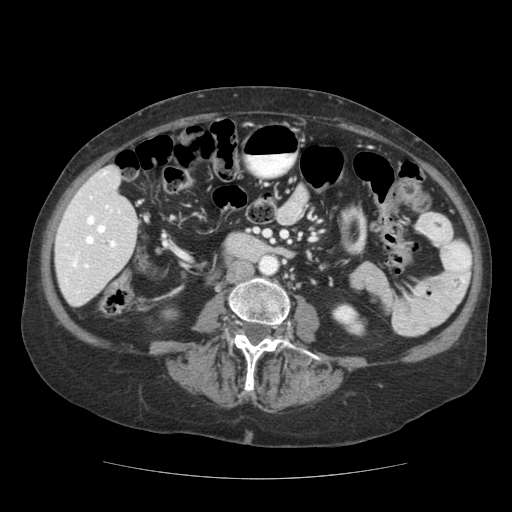
Contrast-enhanced abdominal CT (liver protocol), one axial slice. Slice 41 of 111 in the series (ordered by position). Soft-tissue window (W 400 / L 40 HU). 512 × 512 image matrix, field of view 360 × 360 mm. Case-level facts recorded for this patient, not image findings: diagnosis: hepatocellular carcinoma (patient treated with transarterial chemoembolisation; whether this scan precedes or follows treatment is not stated here); TNM stage (as recorded): Stage-I; Child-Pugh class: A; tumour nodularity: uninodular; tumour size: 7.3 cm.
Annotated regions visible in this slice (semi-automatic segmentation, software-assisted and operator-edited):
- liver parenchyma outside the tumour (the mass and vessels are separate outlines, so this box may not span the whole liver): box from (x=54, y=166) to (x=138, y=306) px
- liver vessels: (x=58, y=171)–(x=126, y=293)